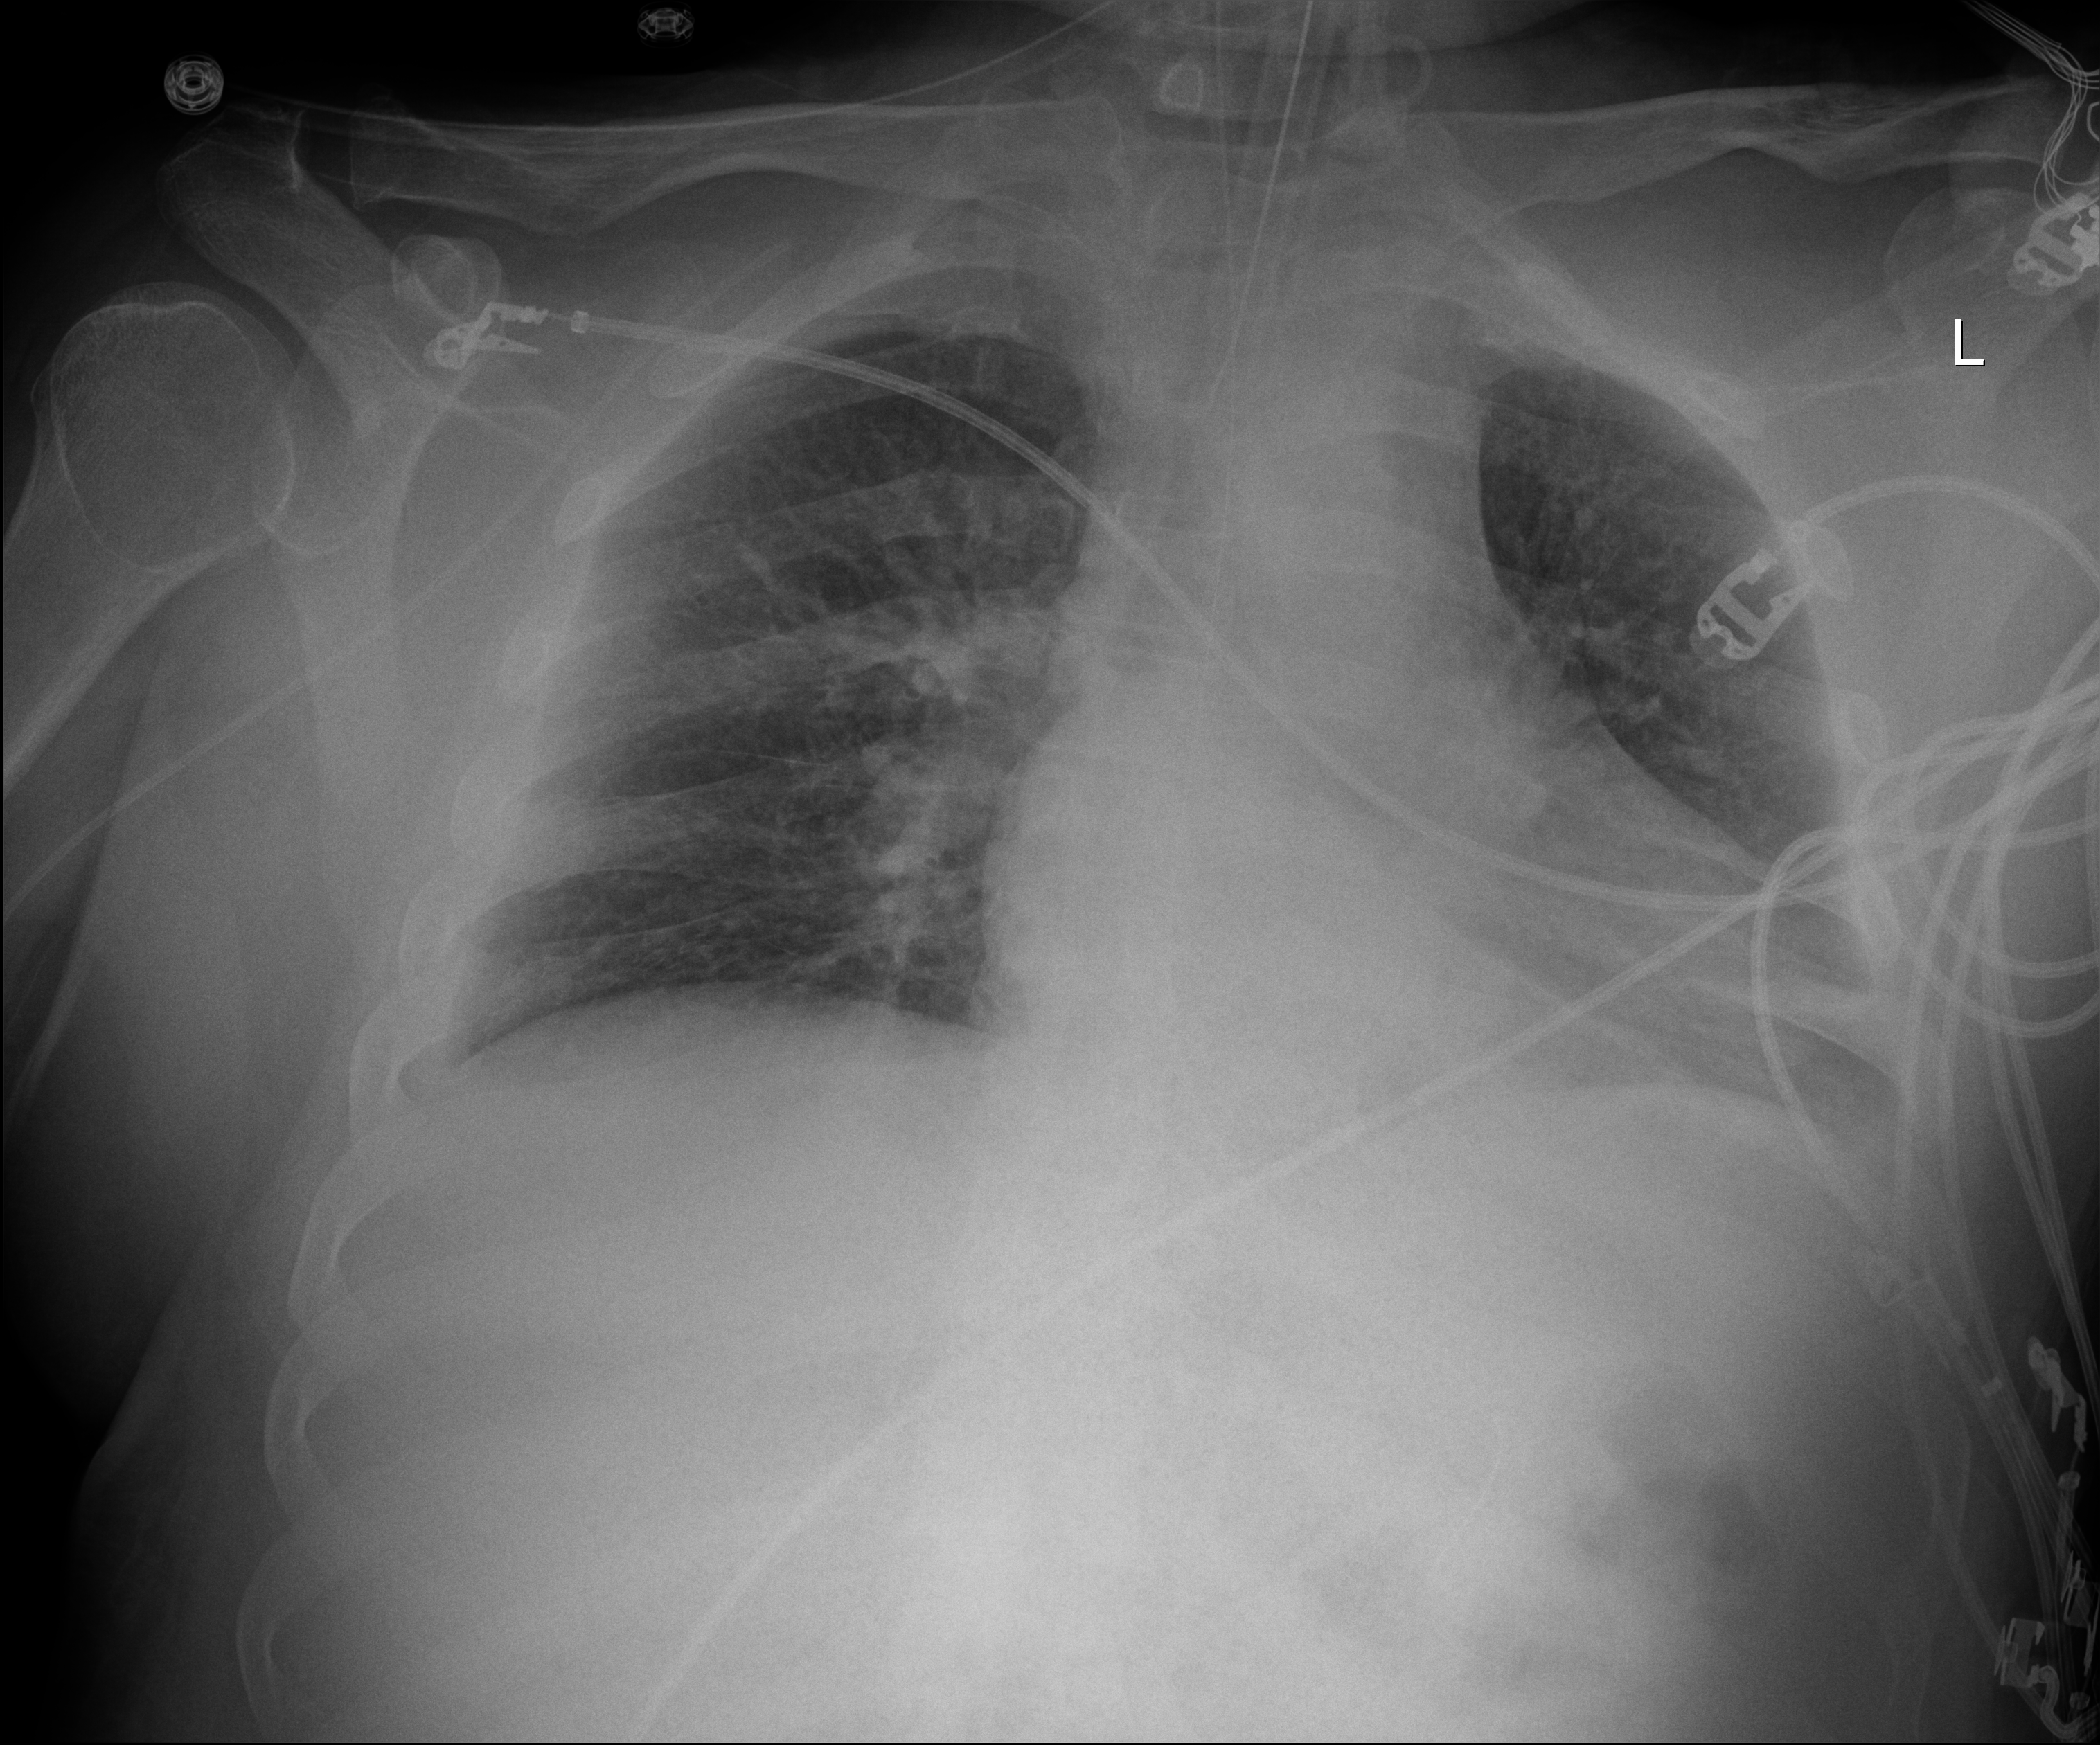
Chest X-ray (portable), anteroposterior (AP) projection. Patient hospitalised with COVID-19; male, aged 18–59 years.
Hospital-stay facts (about this admission, not read from this image; timing relative to this image not recorded): mechanically ventilated during this hospital stay: yes.